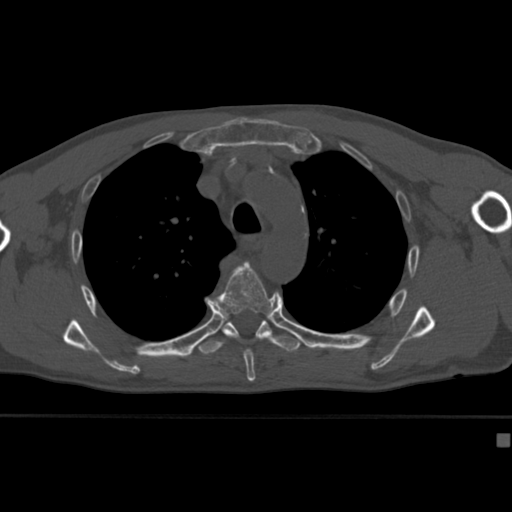
CT including the spine, one axial slice; slice 304 of 430 in the series (ordered by position); reconstruction kernel Br40s; bone window (W 1800 / L 400 HU); 1.5 mm slice thickness; 512 × 512 image matrix, field of view 337 × 337 mm. Patient: male, 64 years. From the clinical record (not read from this slice): primary cancer: uterus; vertebrae with lytic lesions (as recorded): T1, T4, T5, T7, L5.
Structures marked on this image (semi-automatic segmentation, software-assisted and operator-edited):
- T5 vertebra: bounding box [x1, y1, x2, y2] px = [207, 261, 275, 382]
- T6 vertebra: [199, 320, 301, 355]